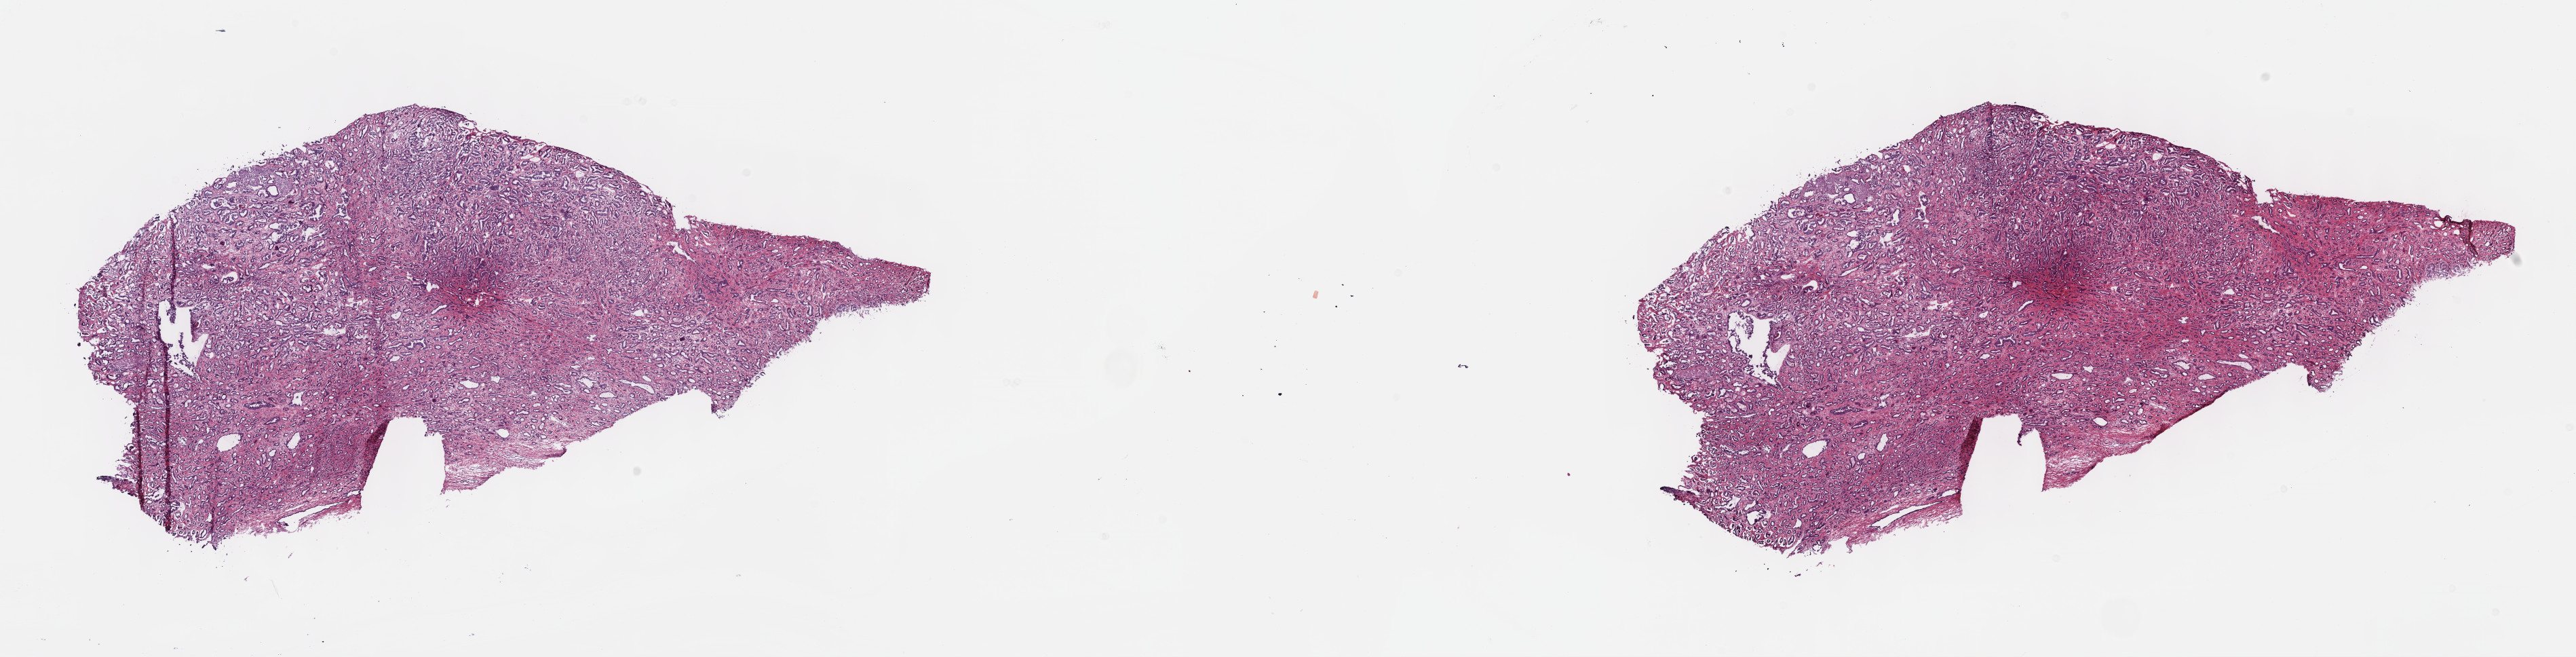
Hematoxylin and eosin (H&E) stained whole-slide image, low-resolution overview of the scanned area, about 30.7 x 7.8 mm (acquisition: 40x scan). Frozen section. Prostate, primary tumour sample. Patient: male, age at initial diagnosis 55 years. Composition of this section per pathologist review: tumour cells 70%, tumour nuclei 70%.
Pathologic diagnosis: Adenocarcinoma, NOS (prostate gland).